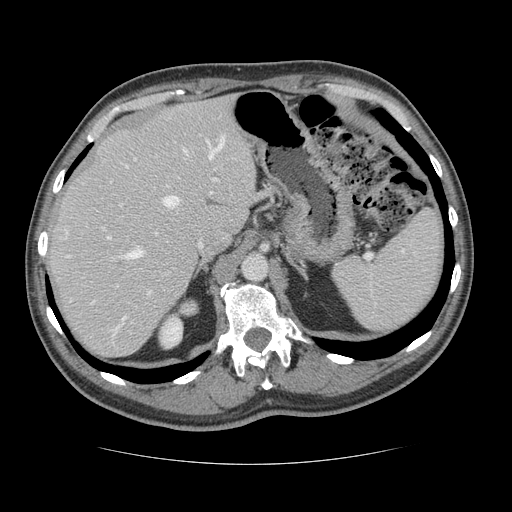
Contrast-enhanced abdominal CT, one axial slice; slice 92 of 134 in the series (ordered by position); intravenous contrast given; soft-tissue window (W 400 / L 40 HU); 512 × 512 image matrix. Male patient, age 68 years. From the clinical record (not read from this slice): diagnosis: colorectal cancer liver metastases, imaged before liver resection; multiple liver metastases: yes; largest metastasis: 2.2 cm.
Structures marked on this image (manually delineated by an expert):
- hepatic veins: bounding box [x1, y1, x2, y2] px = [114, 135, 225, 334]
- liver: [47, 98, 257, 359]
- planned liver remnant (the part of the liver to remain after resection): [47, 98, 257, 335]
- portal vein (with intrahepatic branches): [104, 141, 219, 294]